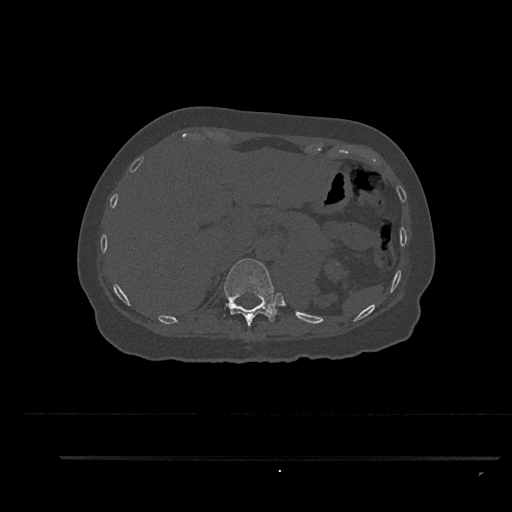
CT including the spine, one axial slice; slice 315 of 797 in the series (ordered by position); bone window (W 1800 / L 400 HU); 0.5 mm slice thickness; 512 × 512 image matrix, field of view 408 × 408 mm. Patient: female, 44 years. Case-level facts recorded for this patient, not image findings: primary cancer: renal; vertebrae with lytic lesions (as recorded): L1.
Annotated regions visible in this slice (semi-automatically segmented with operator editing):
- T11 vertebra: bounding box [x1, y1, x2, y2] px = [224, 259, 280, 326]